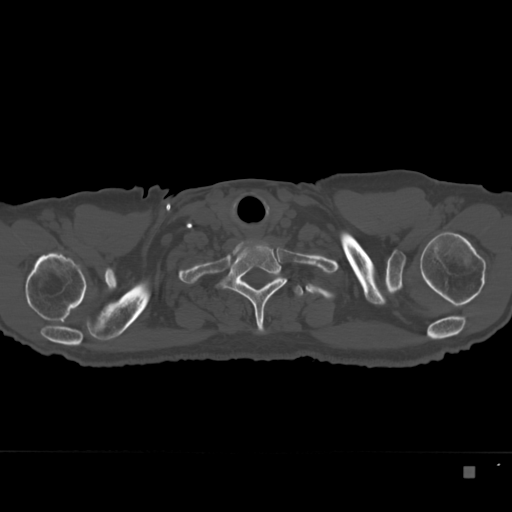
CT including the spine, one axial slice; slice 315 of 332 in the series (ordered by position); reconstruction kernel Br40s; 120 kVp; bone window (W 1800 / L 400 HU); 1.5 mm slice thickness; 512 × 512 image matrix. Male patient, age 72 years. From the clinical record (not read from this slice): primary cancer: skeletal.
Structures marked on this image (semi-automatic segmentation, software-assisted and operator-edited):
- T1 vertebra: bounding box <219,241,287,333> (left, top, right, bottom; pixels)
- T2 vertebra: <244,282,304,296>